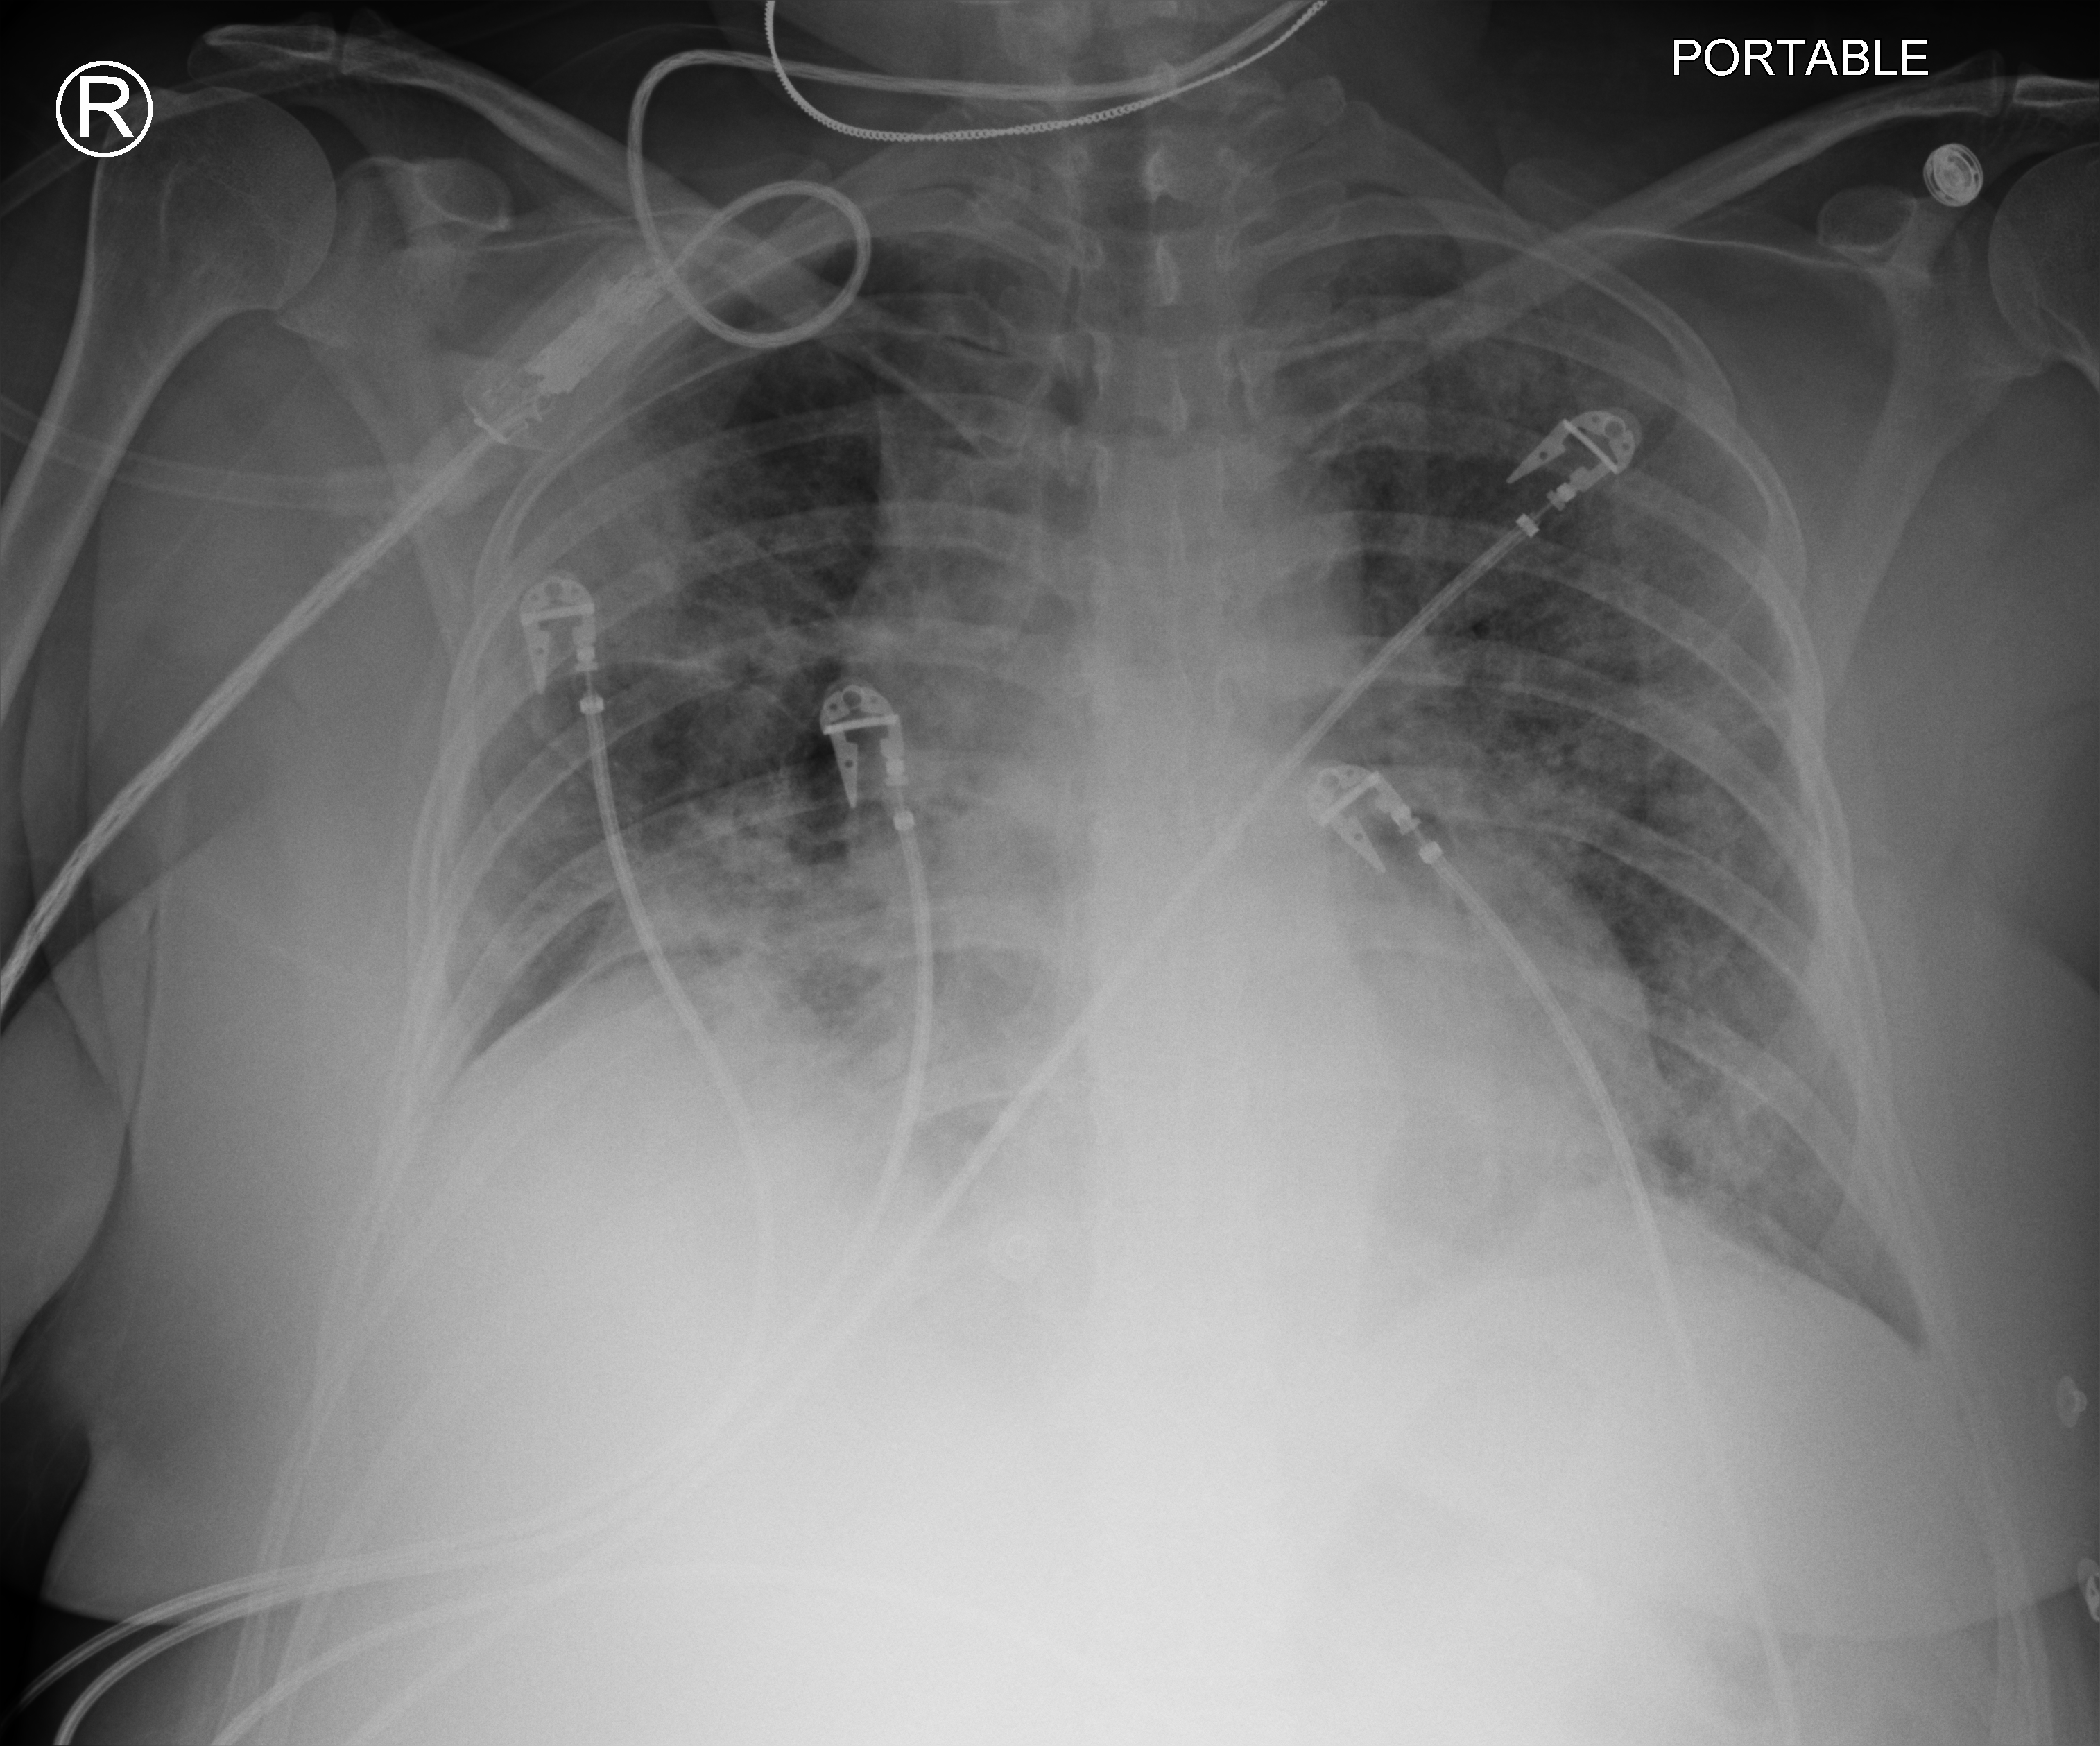
Chest X-ray (portable), anteroposterior (AP) projection. Patient hospitalised with COVID-19; female, aged 18–59 years.
Hospital-stay facts (about this admission, not read from this image; timing relative to this image not recorded): admitted to intensive care during this hospital stay: yes.